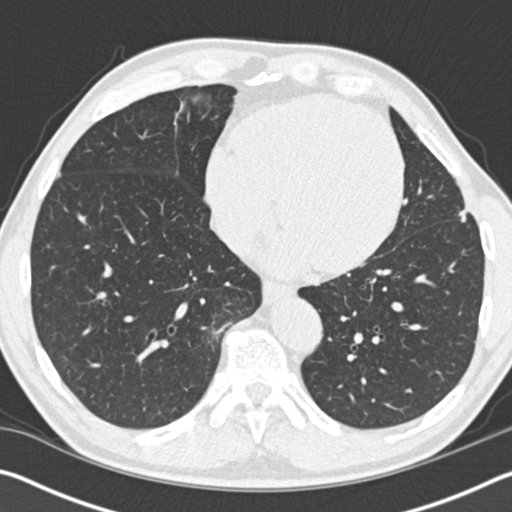
Low-dose screening chest CT, one axial slice; position 50 of 162 along the scan axis; reconstruction kernel B30f; 120 kVp; lung window (W 1500 / L -600 HU); 512 × 512 image matrix.
Annotated regions visible in this slice (expert manual segmentation):
- lesion 1 (tumor, upper lobe of left lung): bounding box <458,209,468,222> (left, top, right, bottom; pixels)